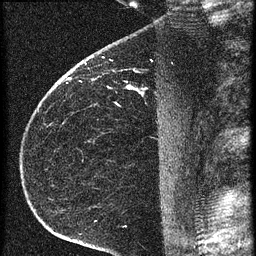
Breast MRI (dynamic contrast-enhanced), one sagittal slice. Slice 44 of 60 in the series (ordered by position). 3 images stored at this slice position (order not interpretable as contrast timing). 1.5 T. TE 4.2 ms, TR 20.4 ms. 1.5 mm slice thickness. 256 × 256 image matrix, field of view 180 × 180 mm. Patient: female, 35 years. Case-level facts recorded for this patient, not image findings: setting: breast cancer imaged before/during neoadjuvant chemotherapy; receptor status: HR-positive, HER2-negative.
Structures marked on this image (semi-automatic segmentation, software-assisted and operator-edited):
- analysis volume of interest (the breast-tissue region the enhancement analysis was run in; not a lesion): bounding box [x1, y1, x2, y2] px = [65, 60, 169, 119]
- tumour enhancement mask (voxels above the 90 % enhancement threshold inside the analysis volume of interest): [129, 86, 132, 89]